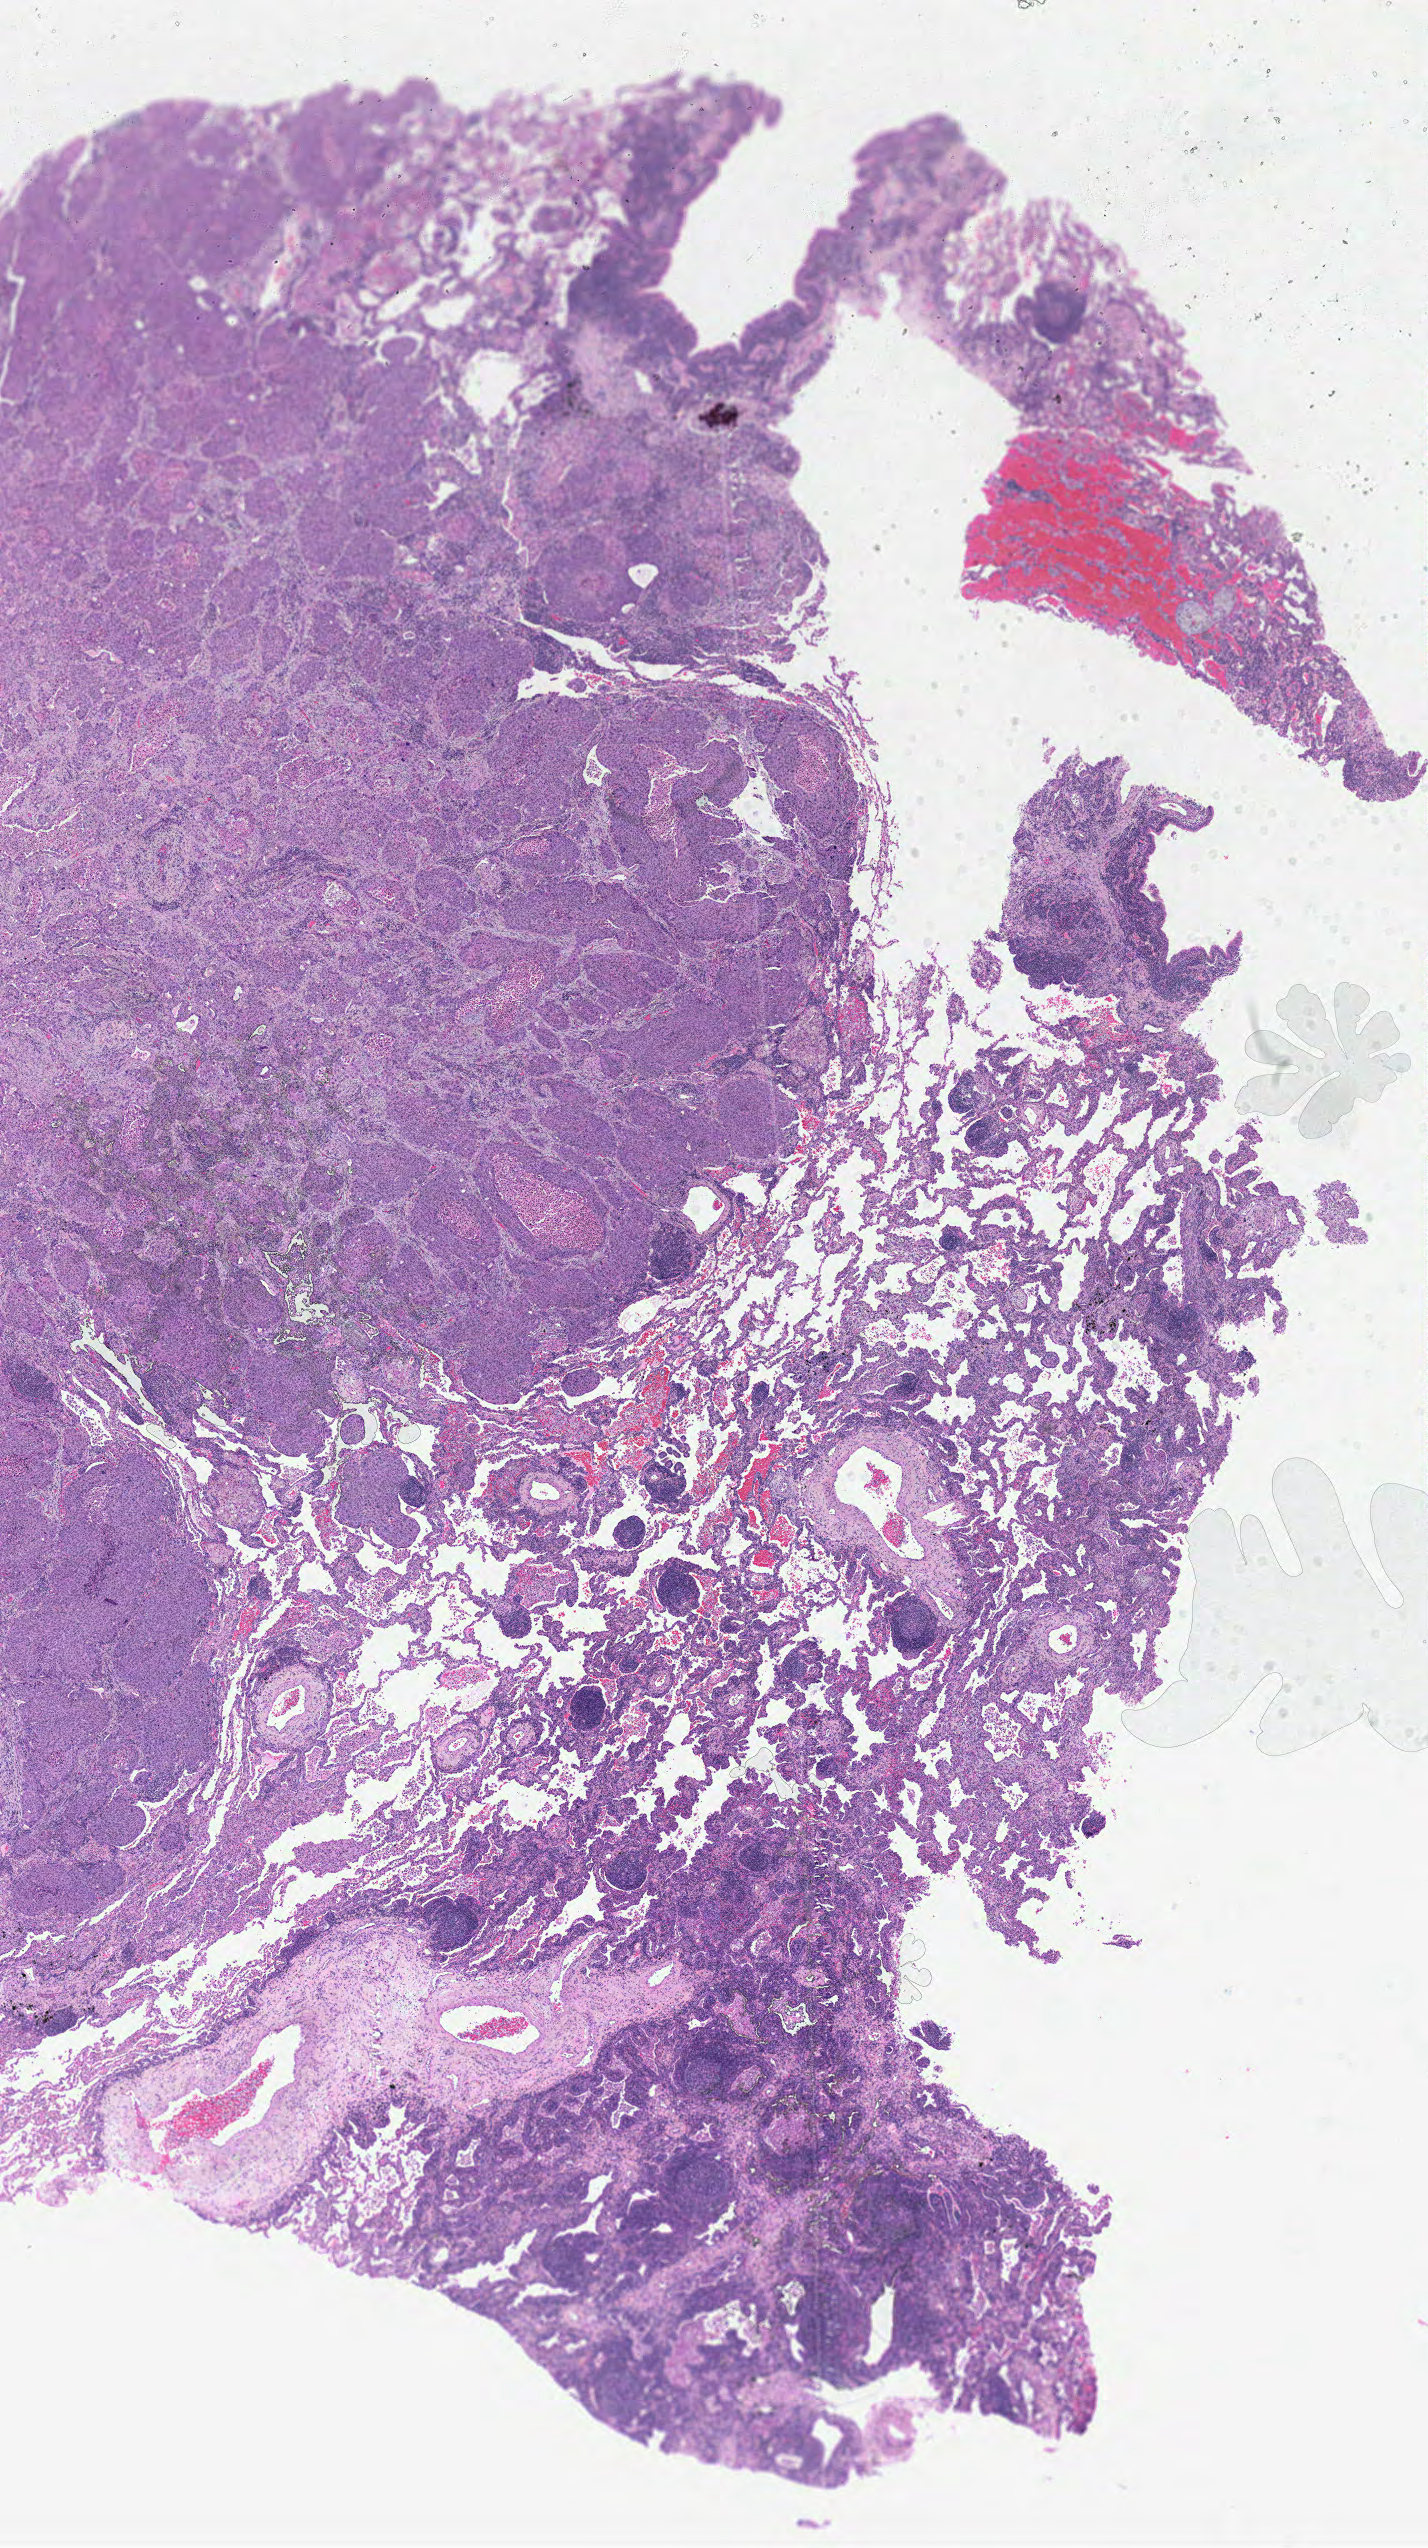
H&E-stained whole-slide image, shown as a low-resolution overview of the whole scanned area (about 11.3 x 20.1 mm, acquisition: 40x scan); formalin-fixed paraffin-embedded (FFPE) diagnostic section; sample: primary tumour, lung. Male patient; age at initial diagnosis 72 years.
TNM: T2 N1 M0. Pathologic diagnosis: Squamous cell carcinoma, NOS (middle lobe, lung). Laterality: right. AJCC pathologic stage: IIB (5th edition).